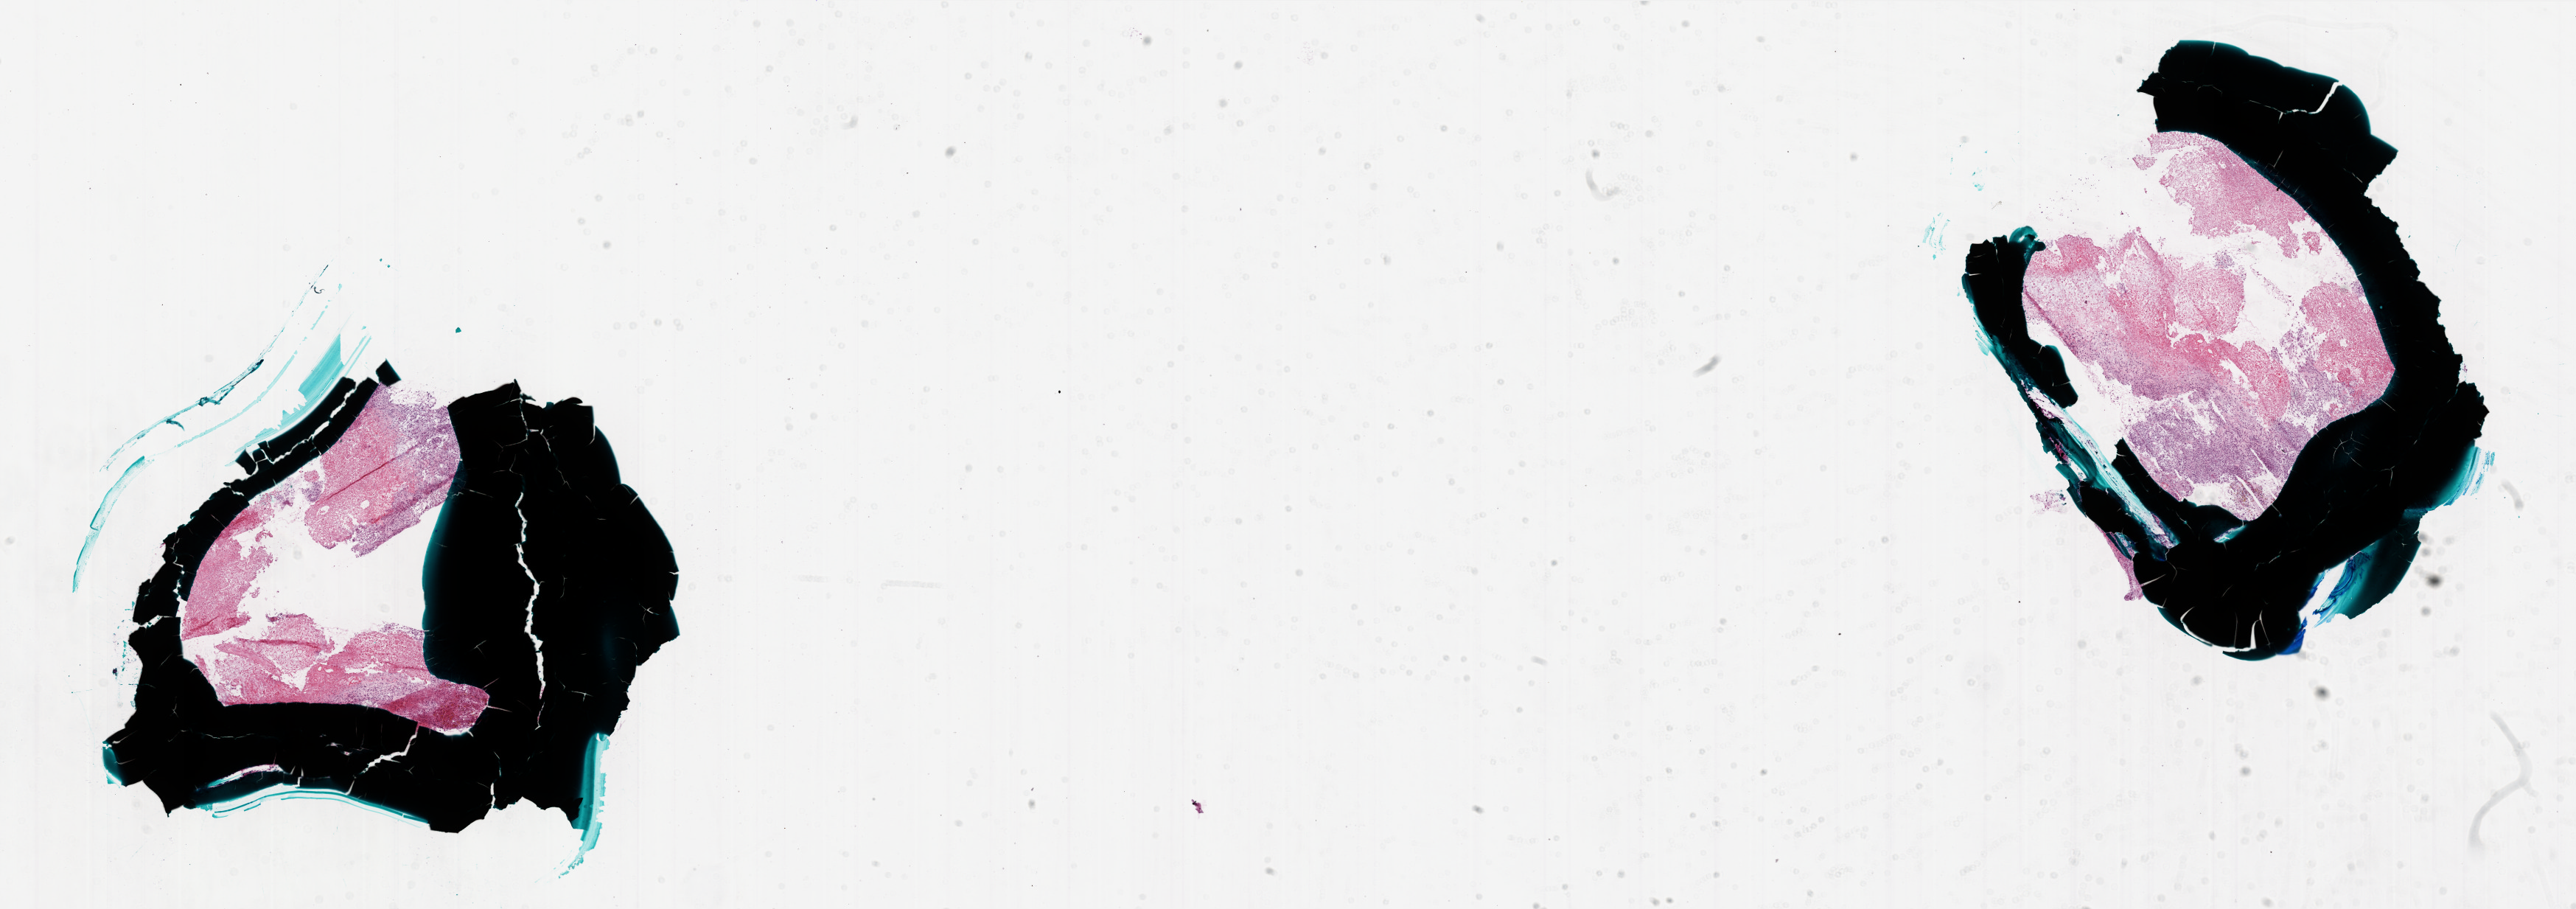
Hematoxylin and eosin (H&E) stained whole-slide image — whole scanned area (about 28.0 x 9.9 mm, acquisition: 20x scan) shown as a low-resolution overview, frozen section, brain, primary tumour sample. Patient: male, age at initial diagnosis 74 years. Pathologist review of this section (percent, as recorded): tumour cells 25%, tumour nuclei 100%, normal cells 0%, stromal cells 0%, necrosis 75%.
Pathologic diagnosis: Glioblastoma.